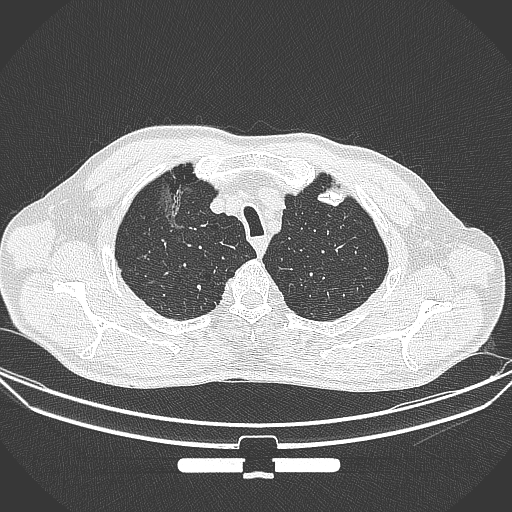
Chest CT, one axial slice. Slice 293 of 355 in the series (ordered by position). Lung window (W 1500 / L -600 HU). 1 mm slice thickness. 512 × 512 image matrix. Male patient, age 67 years. From the clinical record (not read from this slice): clinical TNM (as recorded): T1c N0 M0; histopathological grade: G2.
Structures marked on this image (bounding box drawn by a radiologist):
- lung tumour (recorded histology: adenocarcinoma): bounding box [x1, y1, x2, y2] px = [151, 182, 193, 238]